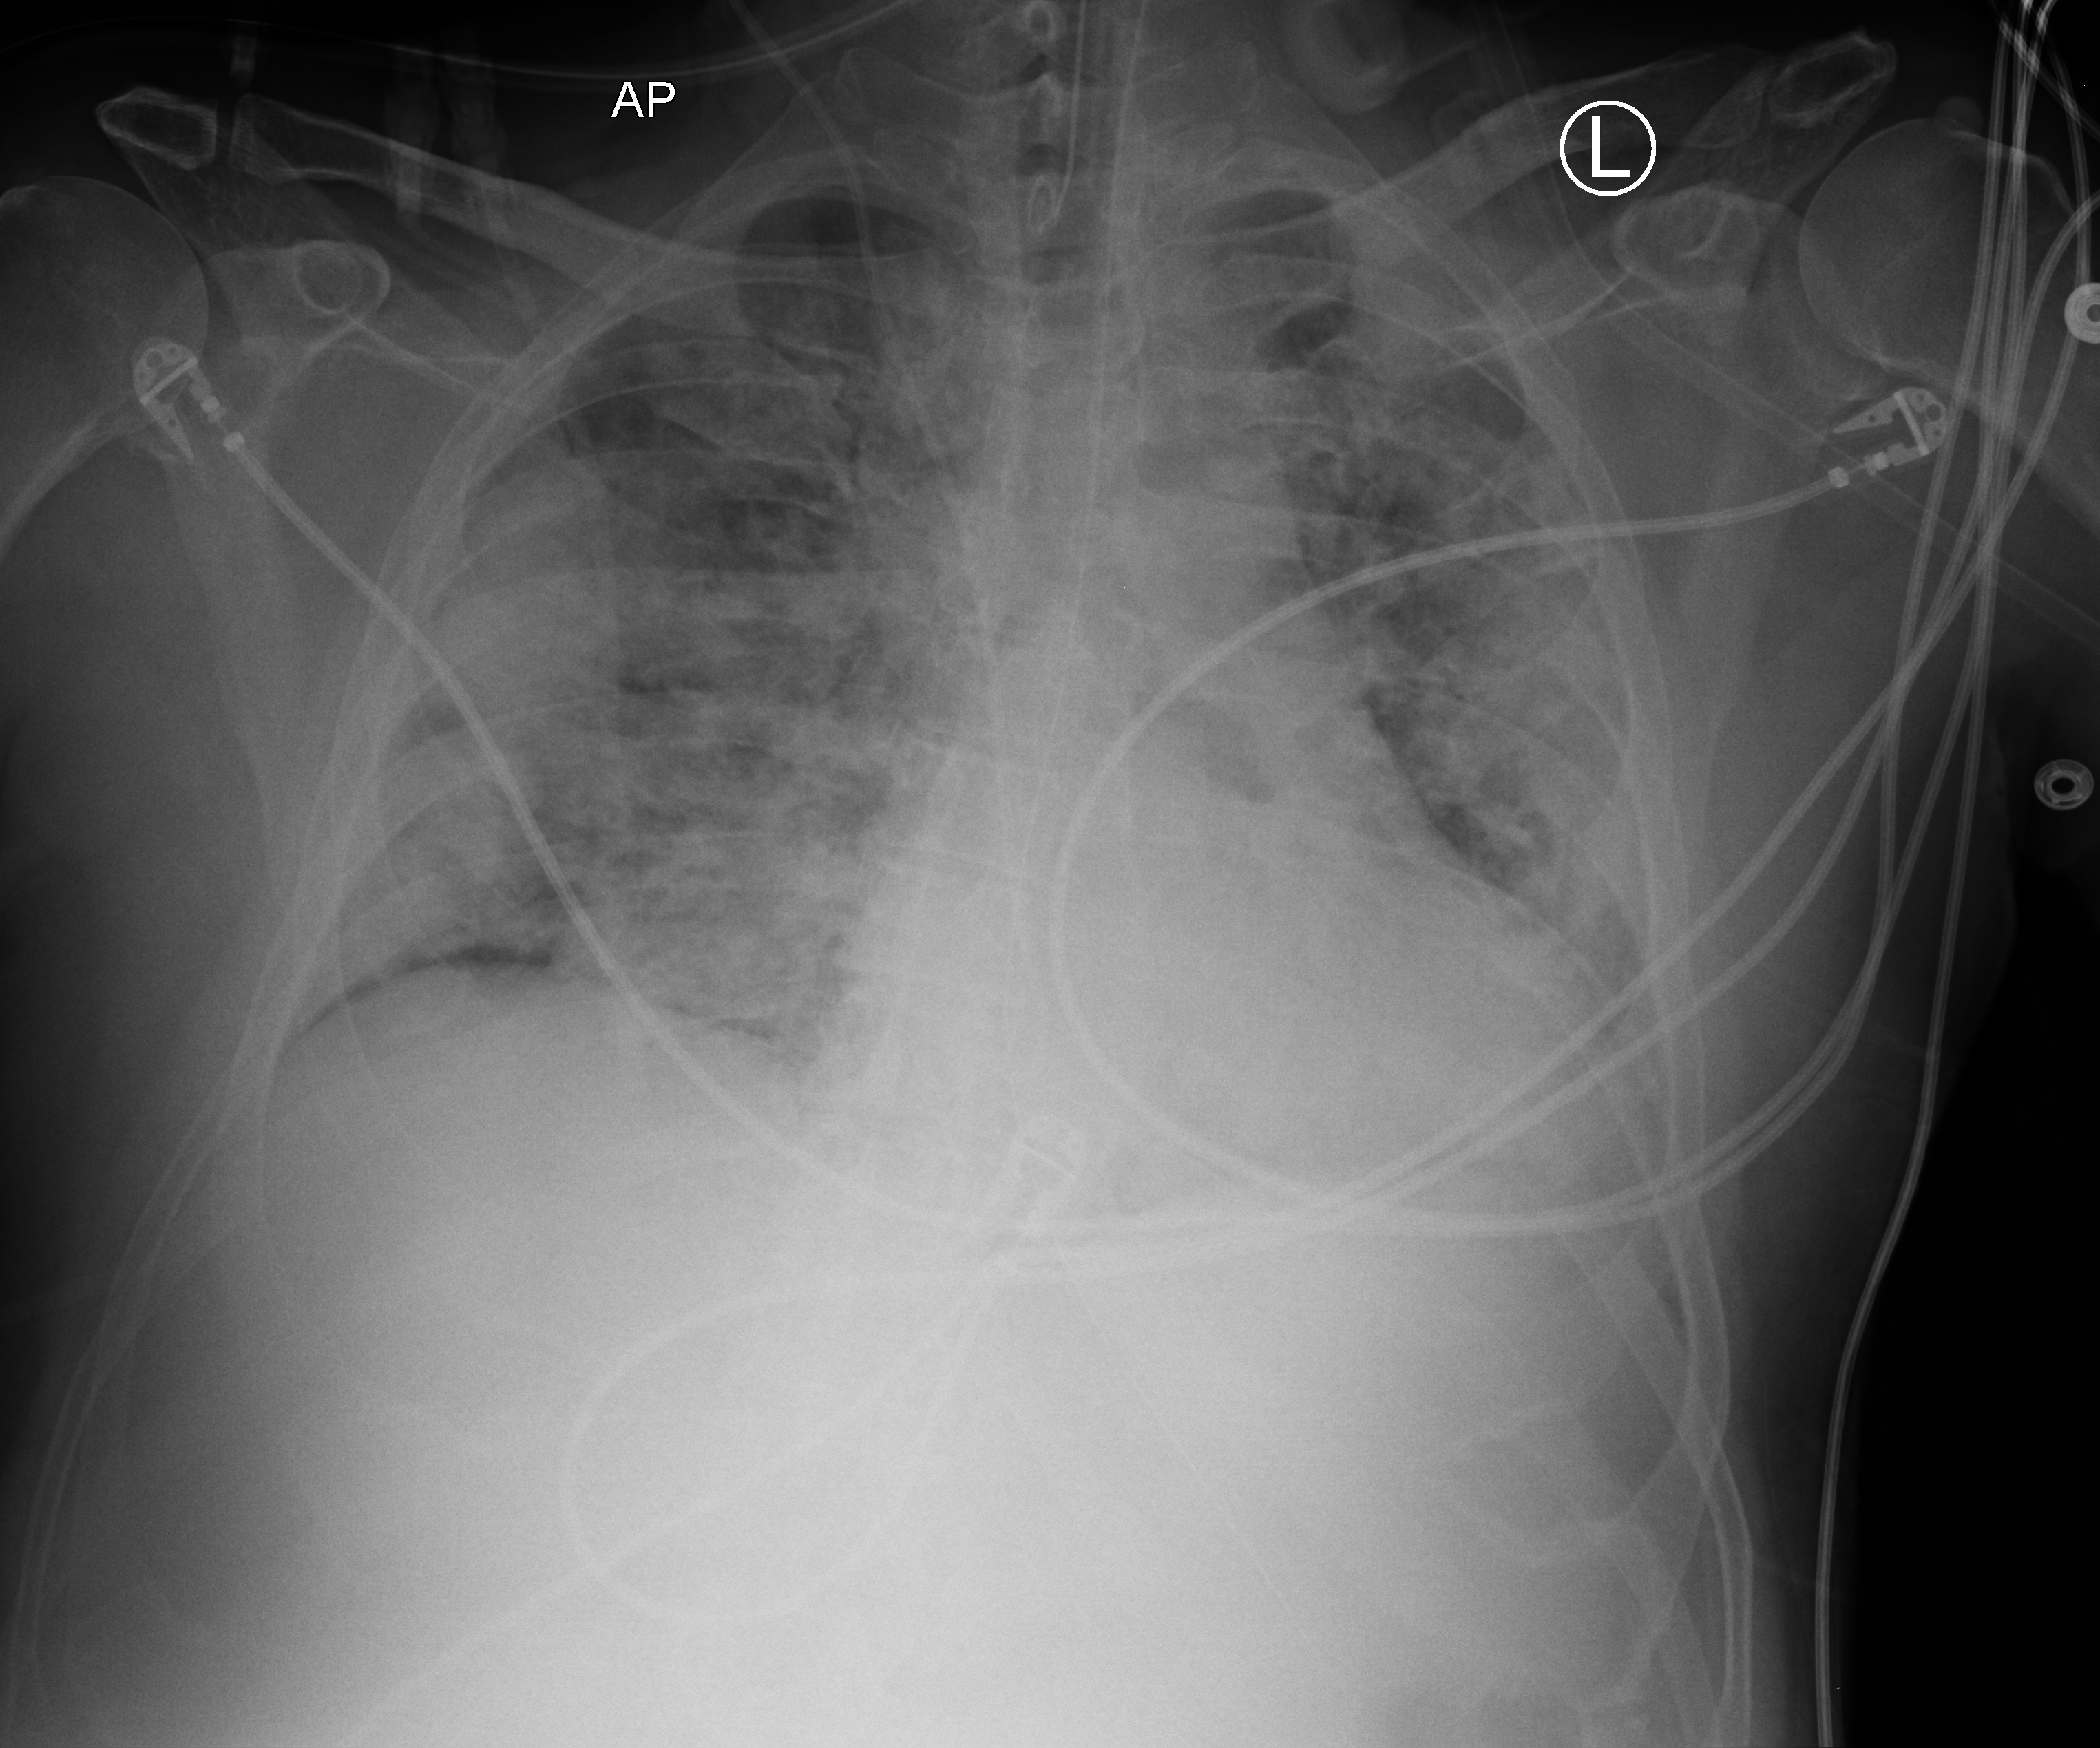
Bedside chest radiograph (computed radiography). Patient hospitalised with COVID-19; male, aged 18–59 years.
From the hospital-stay record, not from the radiograph (when in the stay this image was taken is not recorded):
- admitted to intensive care during this hospital stay: yes
- COPD (admission record): no